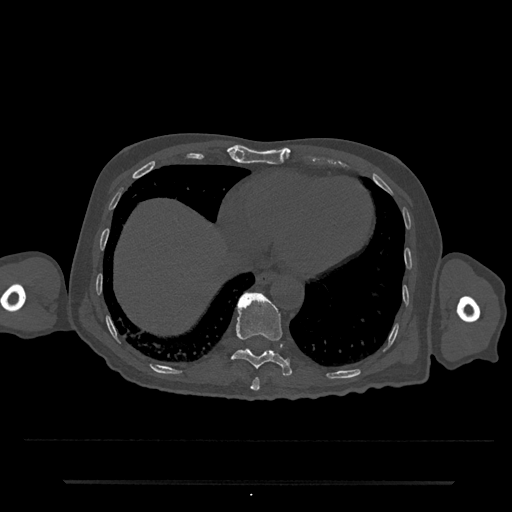
CT including the spine, one axial slice; position 310 of 797 along the scan axis; 120 kVp; bone window (W 1800 / L 400 HU); 512 × 512 image matrix, field of view 427 × 427 mm. Patient: male, 74 years. Case-level facts recorded for this patient, not image findings: primary cancer: prostate.
Structures marked on this image (semi-automatically segmented with operator editing):
- T10 vertebra: bounding box <231,292,292,377> (left, top, right, bottom; pixels)
- T9 vertebra: <250,377,260,391>